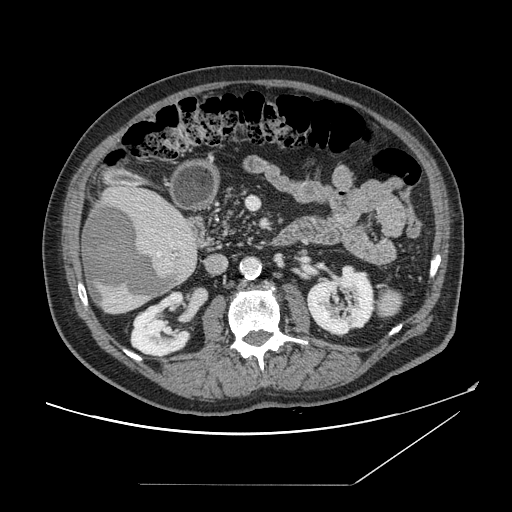
Contrast-enhanced abdominal CT, one axial slice; position 64 of 166 along the scan axis; intravenous contrast given; soft-tissue window (W 400 / L 40 HU); 2.5 mm slice thickness; 512 × 512 image matrix, field of view 416 × 416 mm. Male patient, age 80 years. From the clinical record (not read from this slice): diagnosis: colorectal cancer liver metastases, imaged before liver resection; multiple liver metastases: no; largest metastasis: 2.2 cm; disease in both lobes: no.
Structures marked on this image (expert manual segmentation):
- liver: bounding box <81,186,199,315> (left, top, right, bottom; pixels)
- planned liver remnant (the part of the liver to remain after resection): <125,187,173,211>
- liver metastasis: <84,204,174,307>